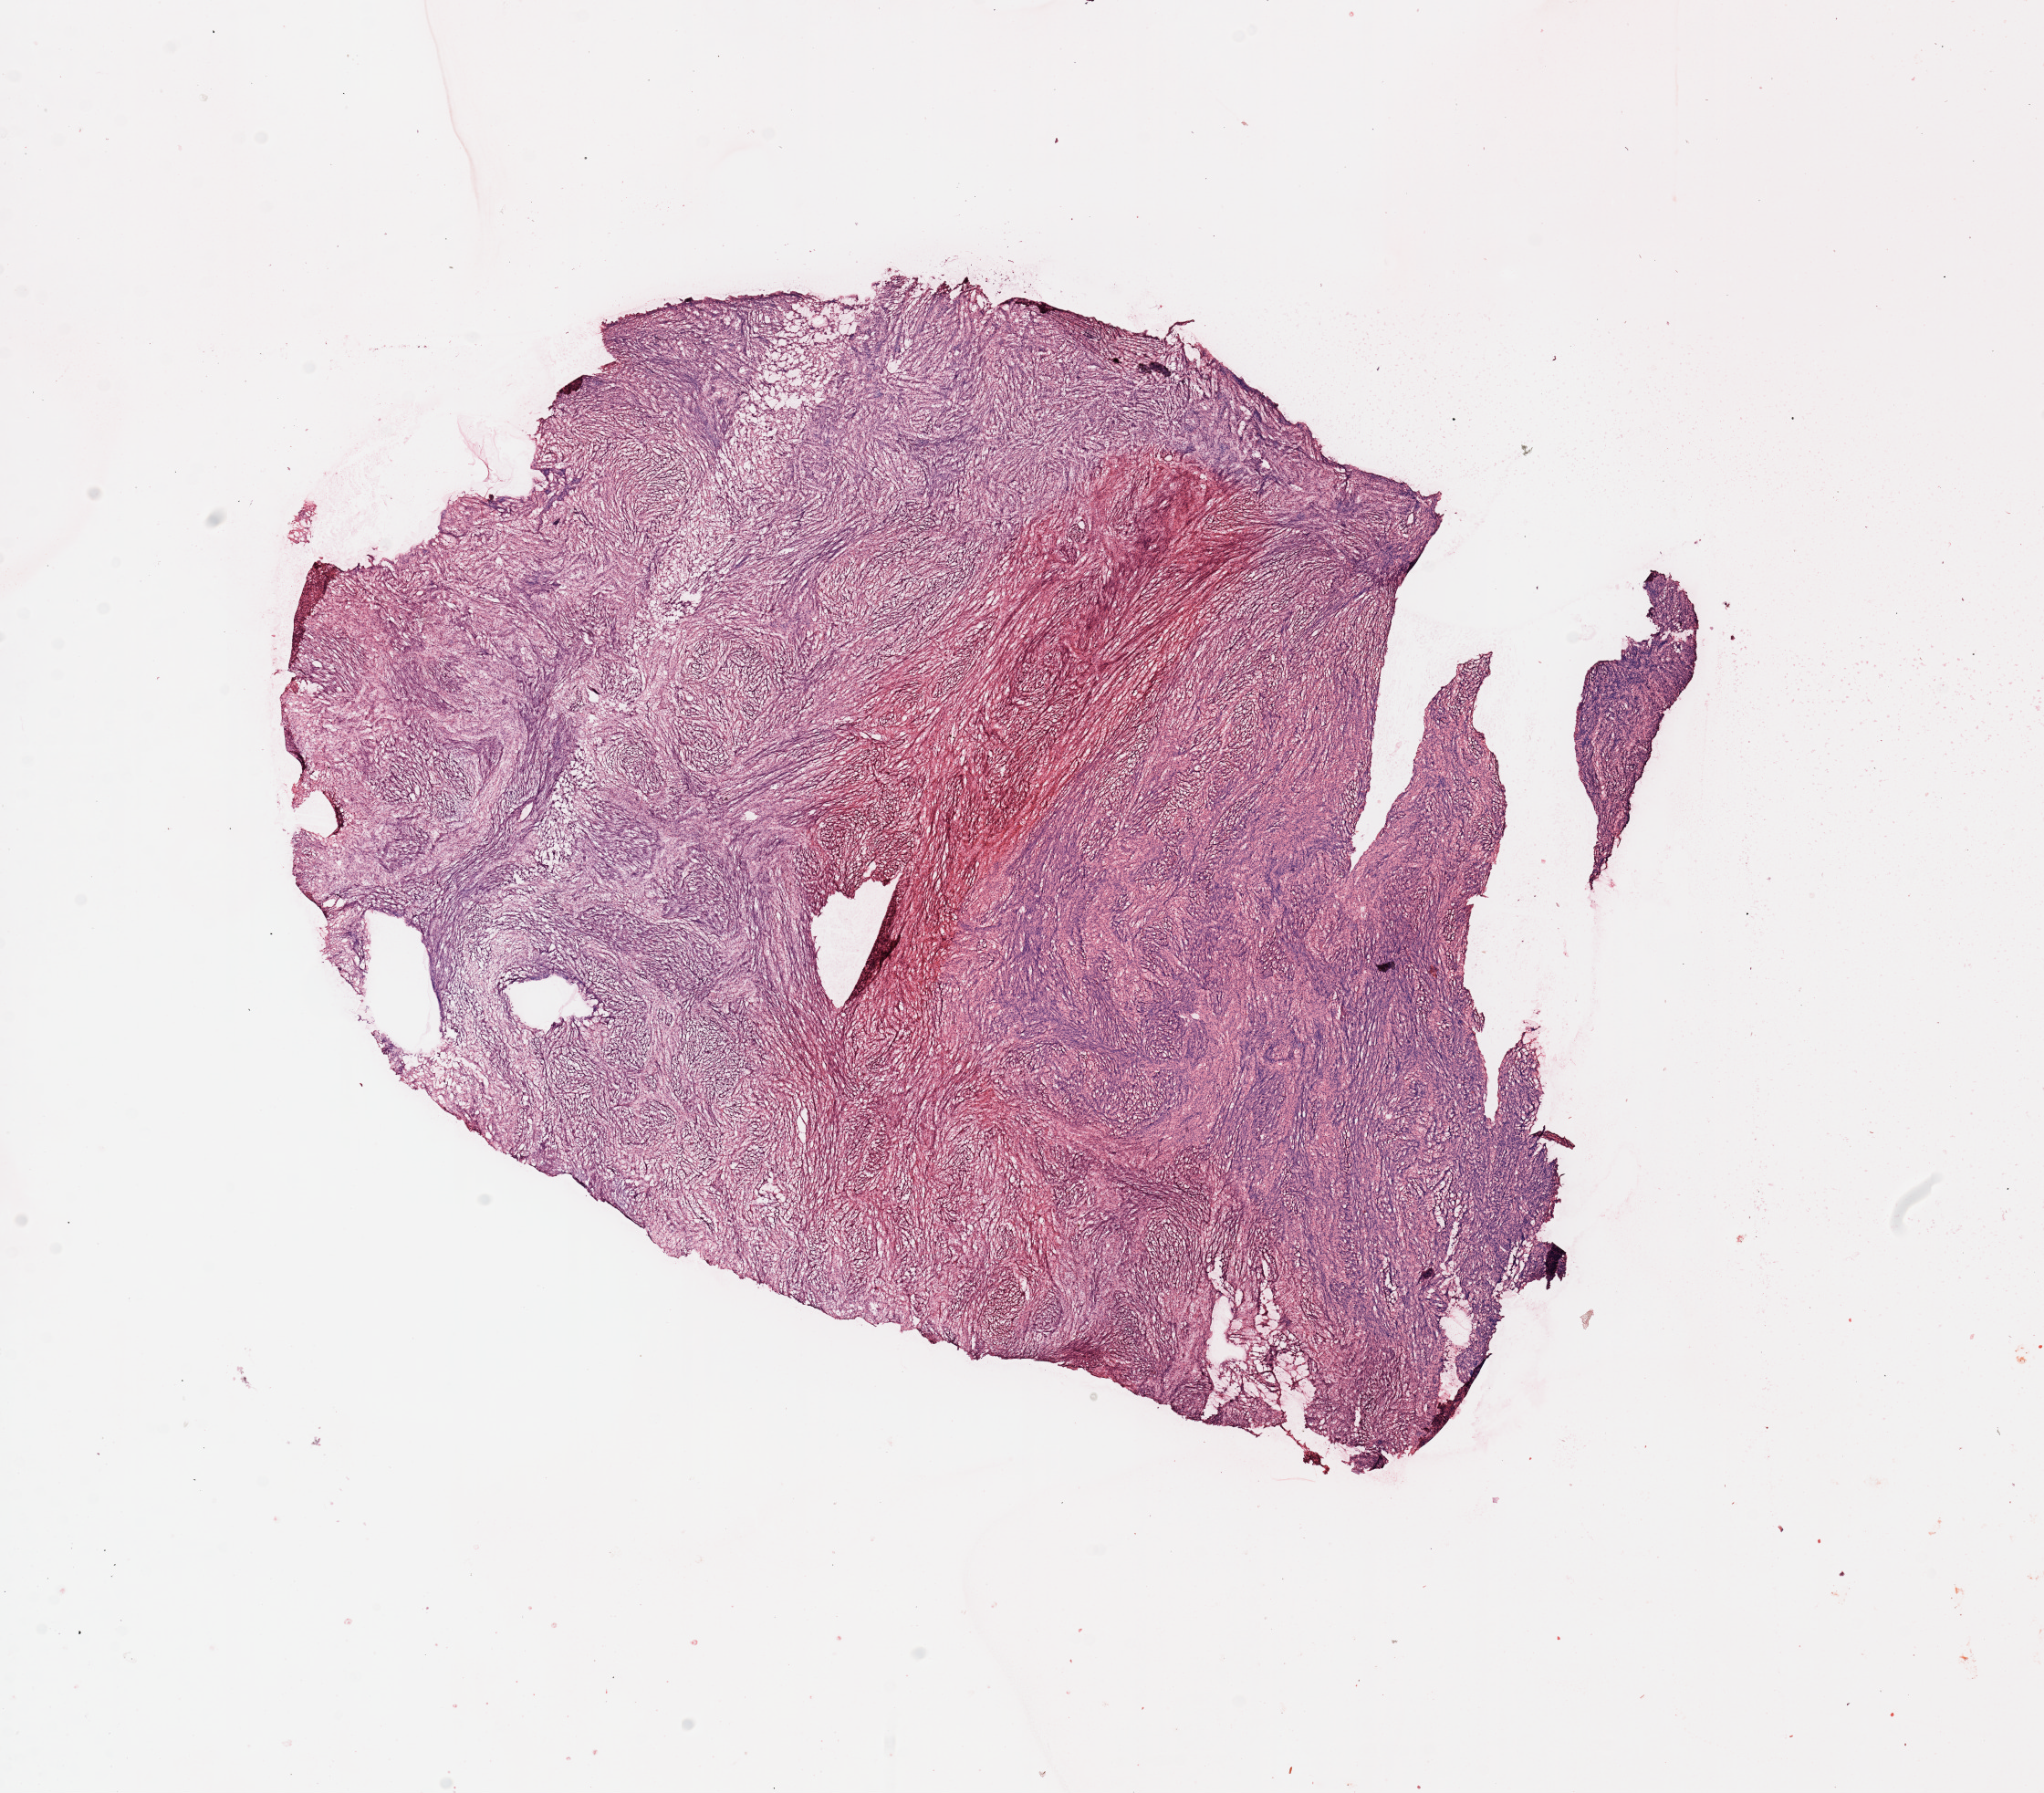
H&E whole-slide image, low-resolution overview of the scanned area, about 17.7 x 15.5 mm. Tumour tissue sample. 42-year-old female patient.
- primary tumour site (as recorded): chest
- patient diagnosis (cohort enrolment): sarcoma (site not recorded at cohort level)